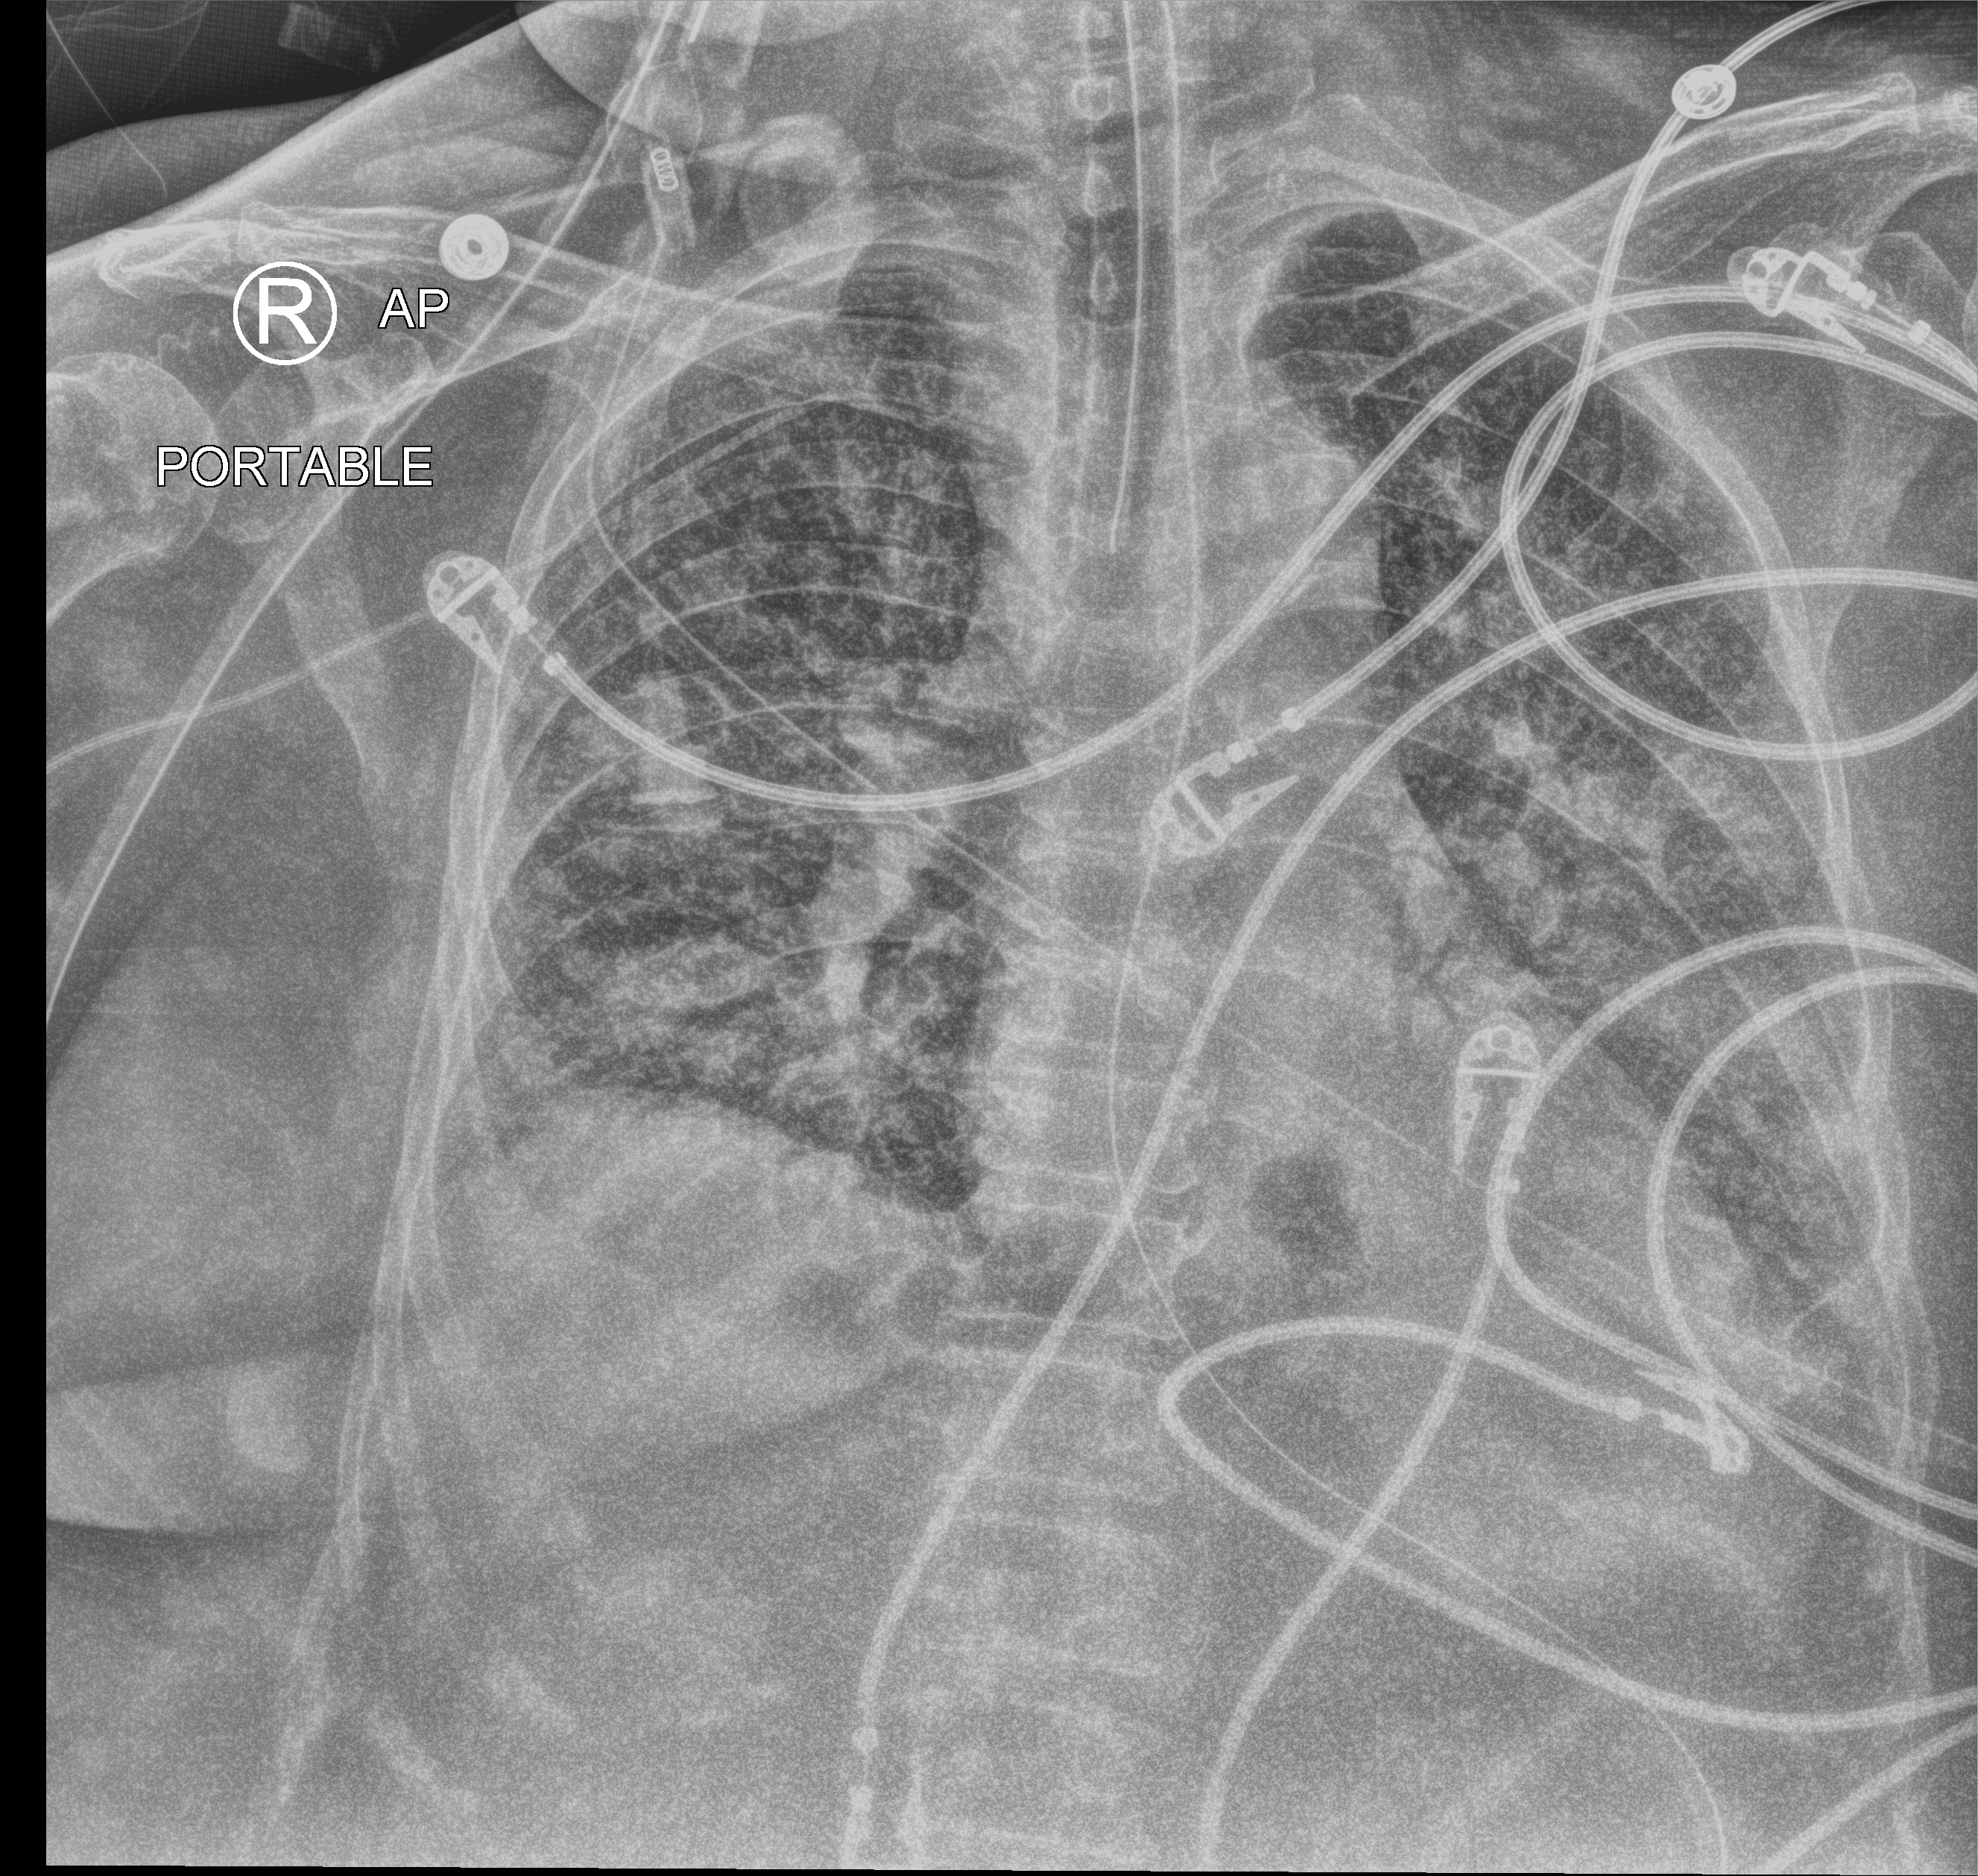
Chest X-ray (portable); anteroposterior (AP) projection. Patient hospitalised with COVID-19; female, aged 60–74 years.
Hospital-stay facts (about this admission, not read from this image; timing relative to this image not recorded): mechanically ventilated during this hospital stay: yes; length of hospital stay: 15 days; COPD (admission record): no.